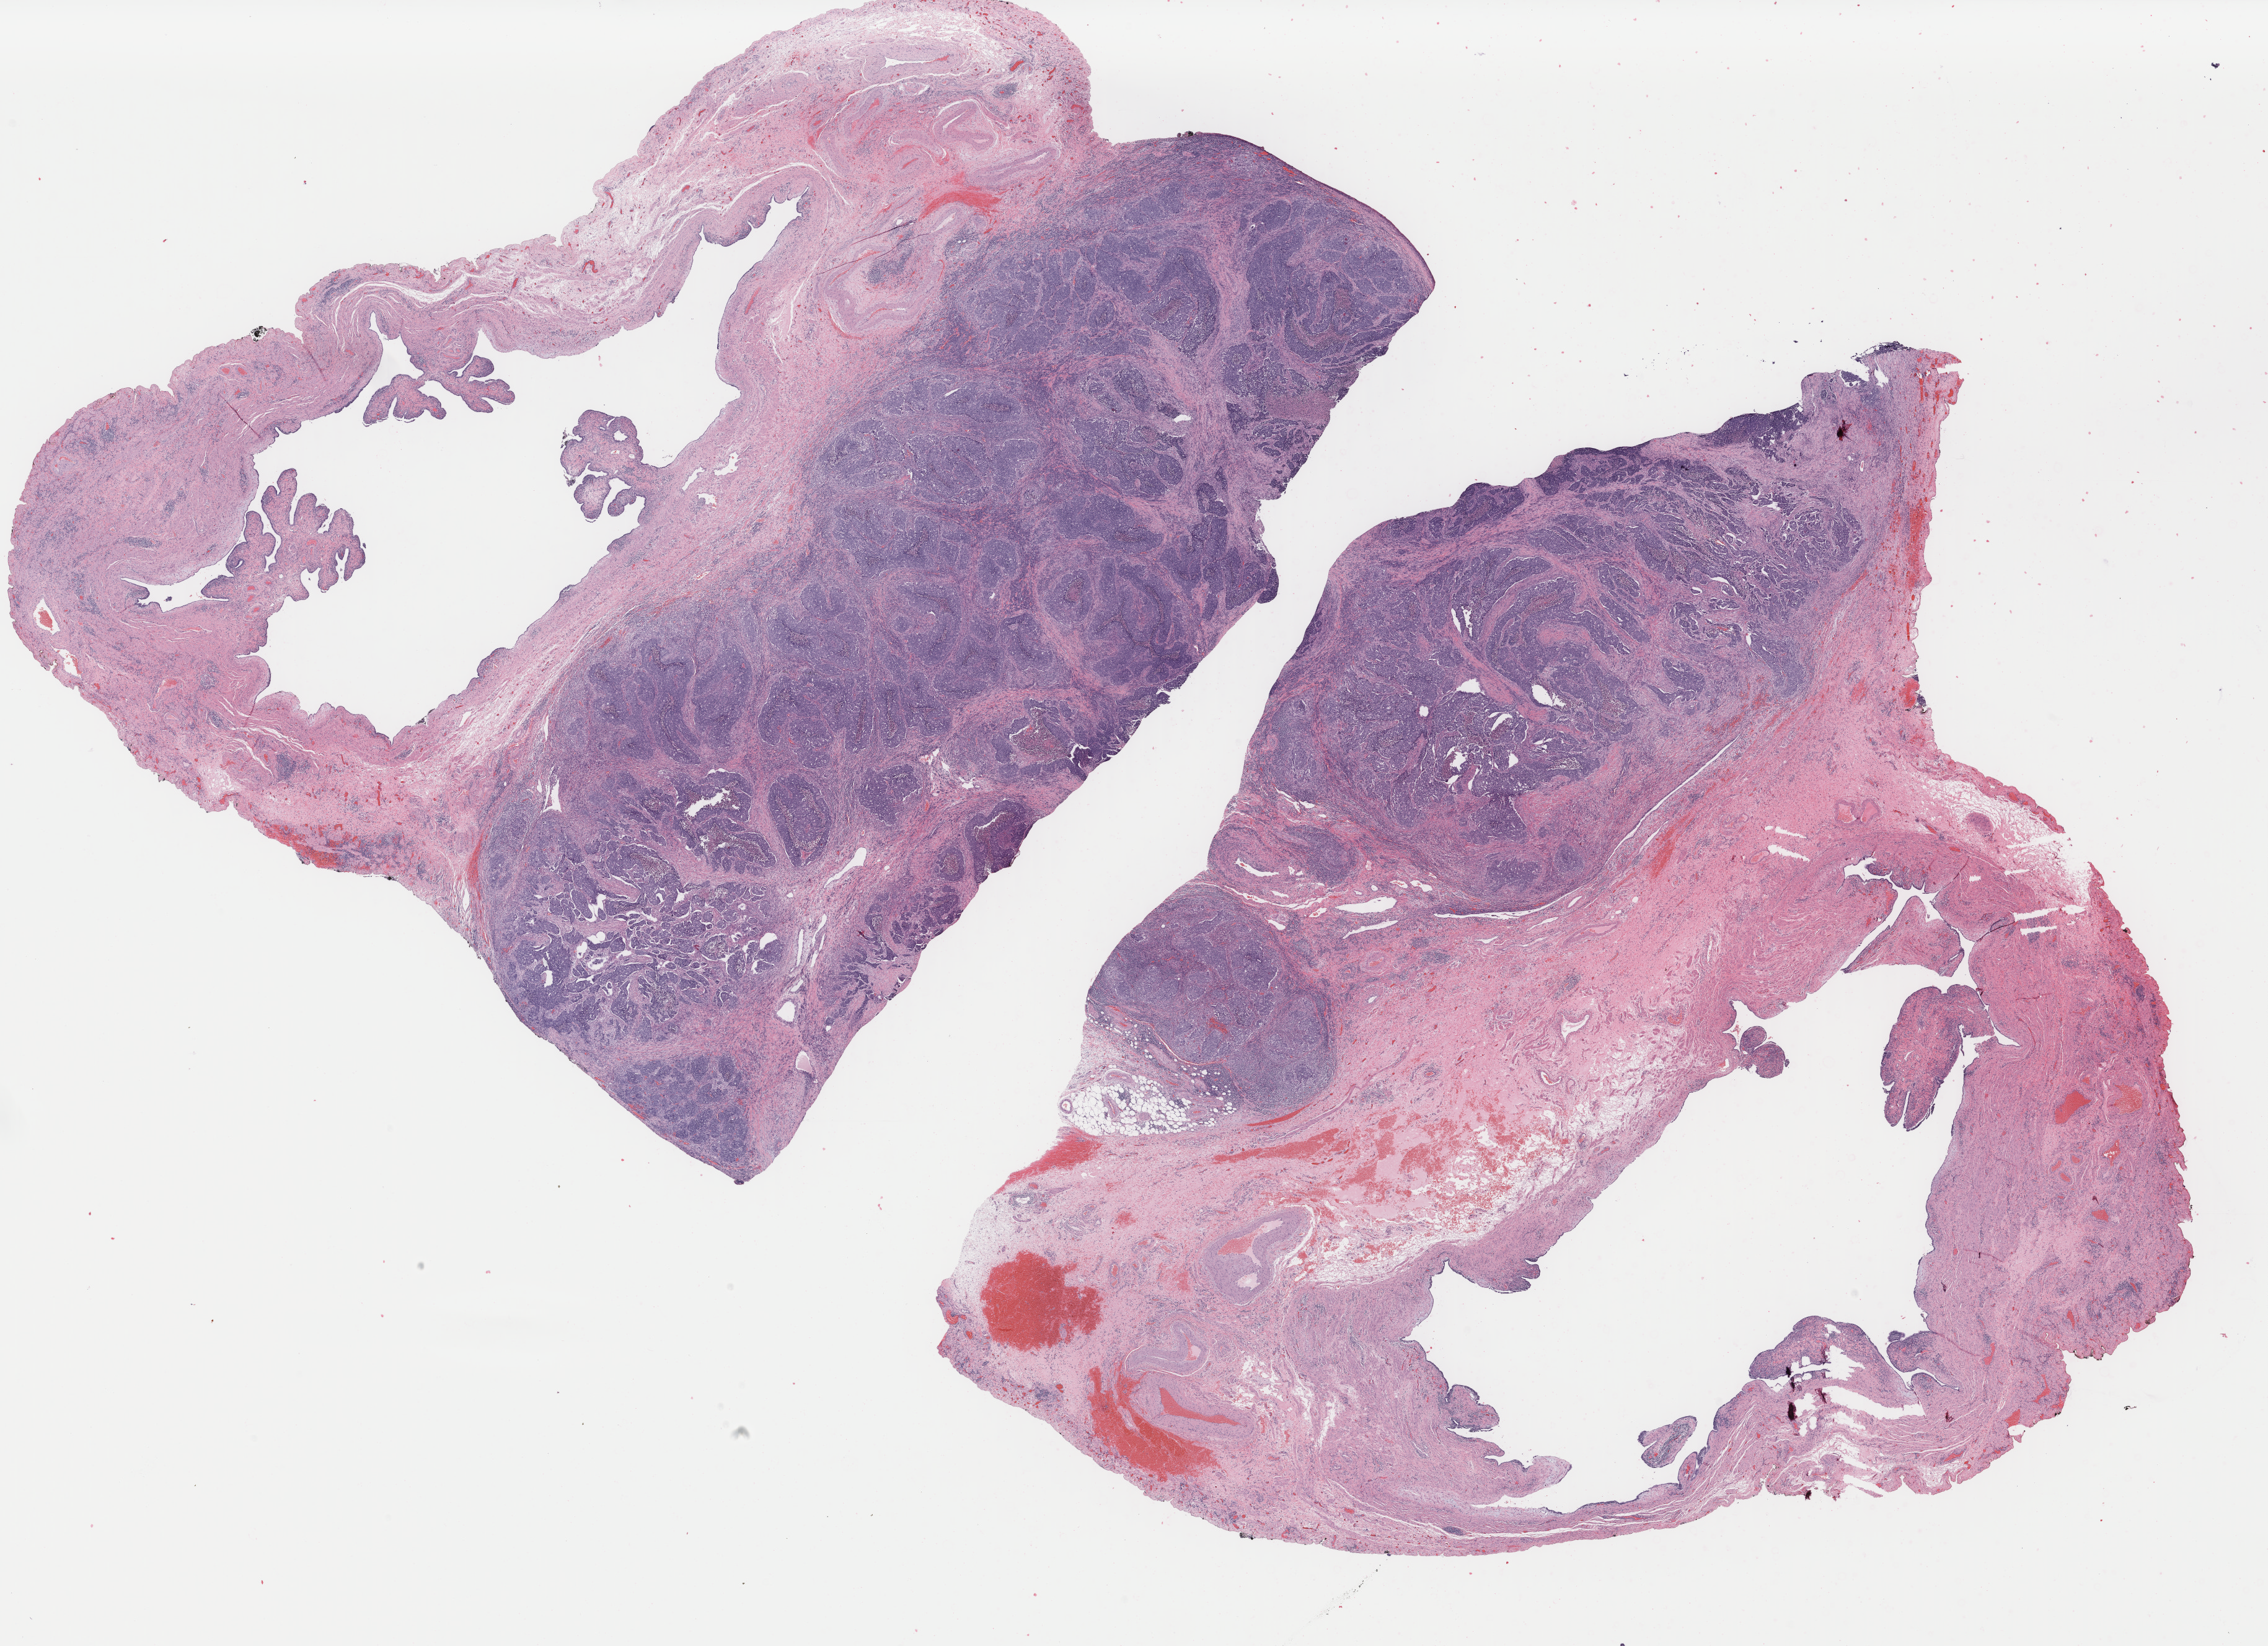
H&E-stained whole-slide image — low-resolution overview of the scanned area, about 29.0 x 21.1 mm (slide scanned at 40x). Formalin-fixed paraffin-embedded (FFPE) diagnostic section. Primary tumour sample from the ovary. Patient: female, age at initial diagnosis 55 years. Histologic grade: G3 (poorly differentiated).
Histologic diagnosis: Serous cystadenocarcinoma, NOS. FIGO stage: IC.